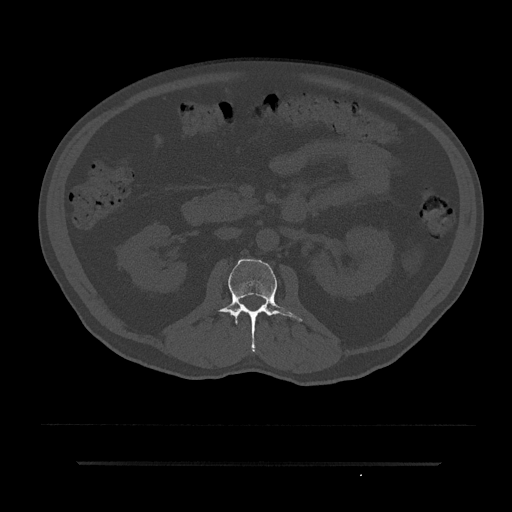
CT including the spine, one axial slice. Position 78 of 797 along the scan axis. Reconstruction kernel Br40s/3. 120 kVp. Bone window (W 1800 / L 400 HU). 512 × 512 image matrix. Male patient, age 59 years. Case-level facts recorded for this patient, not image findings: primary cancer: bile ducts.
Annotated regions visible in this slice (semi-automatic segmentation, software-assisted and operator-edited):
- L1 vertebra: bounding box <240,311,242,313> (left, top, right, bottom; pixels)
- L2 vertebra: <217,258,302,352>